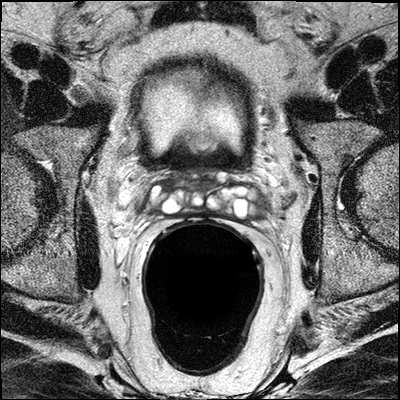
Multiparametric prostate MRI examination; 3 images, each a single mid-volume slice chosen by position (not for content). Treatment context recorded for this patient: No surgery, treated with ADT and definitive RT.
Image 1: T2-weighted axial slice, slice 16 of 30, 3 mm slice thickness.
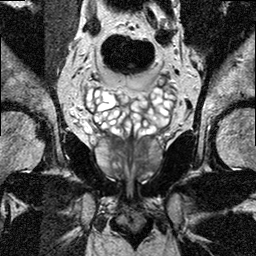
Image 2: coronal T2-weighted image, slice 14 of 26, 3 mm slice thickness.
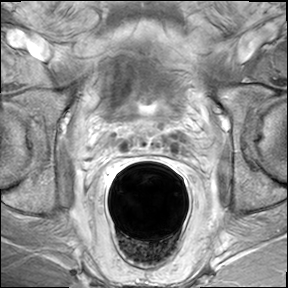
Image 3: DCE (dynamic gadolinium-enhanced) axial slice, series "AX BLISS_GAD_8", slice 16 of 30, dynamic phase 5 of 8.
MRI report (verbatim):
prostate has a maximal lateral diameter of 4.9 cm, a maximal craniocaudal diameter of 3.6 cm and a maximal AP diameter of 3.1 cm resulting in an estimated gland volume of 28 cc. The zonal anatomy is preserved. There is a background of chronic prostatitis. On the T2-weighted images, there is T2 hypointensity from apex to base involving the nearly the entire right peripheral zone. On dynamic contrast-enhanced sequences, there is highly suspicious early wash-in and rapid washout compatible with tumor, which extends to the capsule. At the mid-third level, posterior lateral right at 7 o'clock, there is minimal extracapsular disease with radial extension of up to 1 mm. (series 601, image 11), with possible beginning neurovascular involvement. On the left, the anterior aspect of the peripheral zone from the mid one-third to apical third, there is an area of T2 hypointensity. This region demonstrates highly suspicious contrast enhancement with peak wash in and a rapid wash out suspicious for tumor. This extends to the capsule and there is extracapsular invasion posterior lateral at 5 o'clock, without definite tumor extension beyond the "capsule" (series 601 image 10), at 4 o'clock. In the apex at 3 o'clock possible capsular infiltration without extraprostatic tumor masses. ( as annotated on PACS). No evidence for seminal vesicles infiltration. Seminal vesicles are thin-walled, with intraluminal fluid. No intraluminal masses. No evidence of involvement of bladder neck and rectal wall. No suspiciously enlarged obturator and iliac lymph nodes. IMPRESSION: 1) Bilateral prostate cancer, with highly suspicion of extracapsular extension on the right, and possible beginning extraprostatic extension on the left. (Right peripheral zone infiltration from apex to base with extracapsular extension (radial extension 1 mm) and suspicion for neurovascular bundle involvement. Left anterior peripheral zone tumor from midthird to apical third with possible beginning extracapsular extension at midthird 5 o clock and apex 3 o'clock.) 2) No seminal vesicles involvement. 3) No pelvic lymphadenopathy.